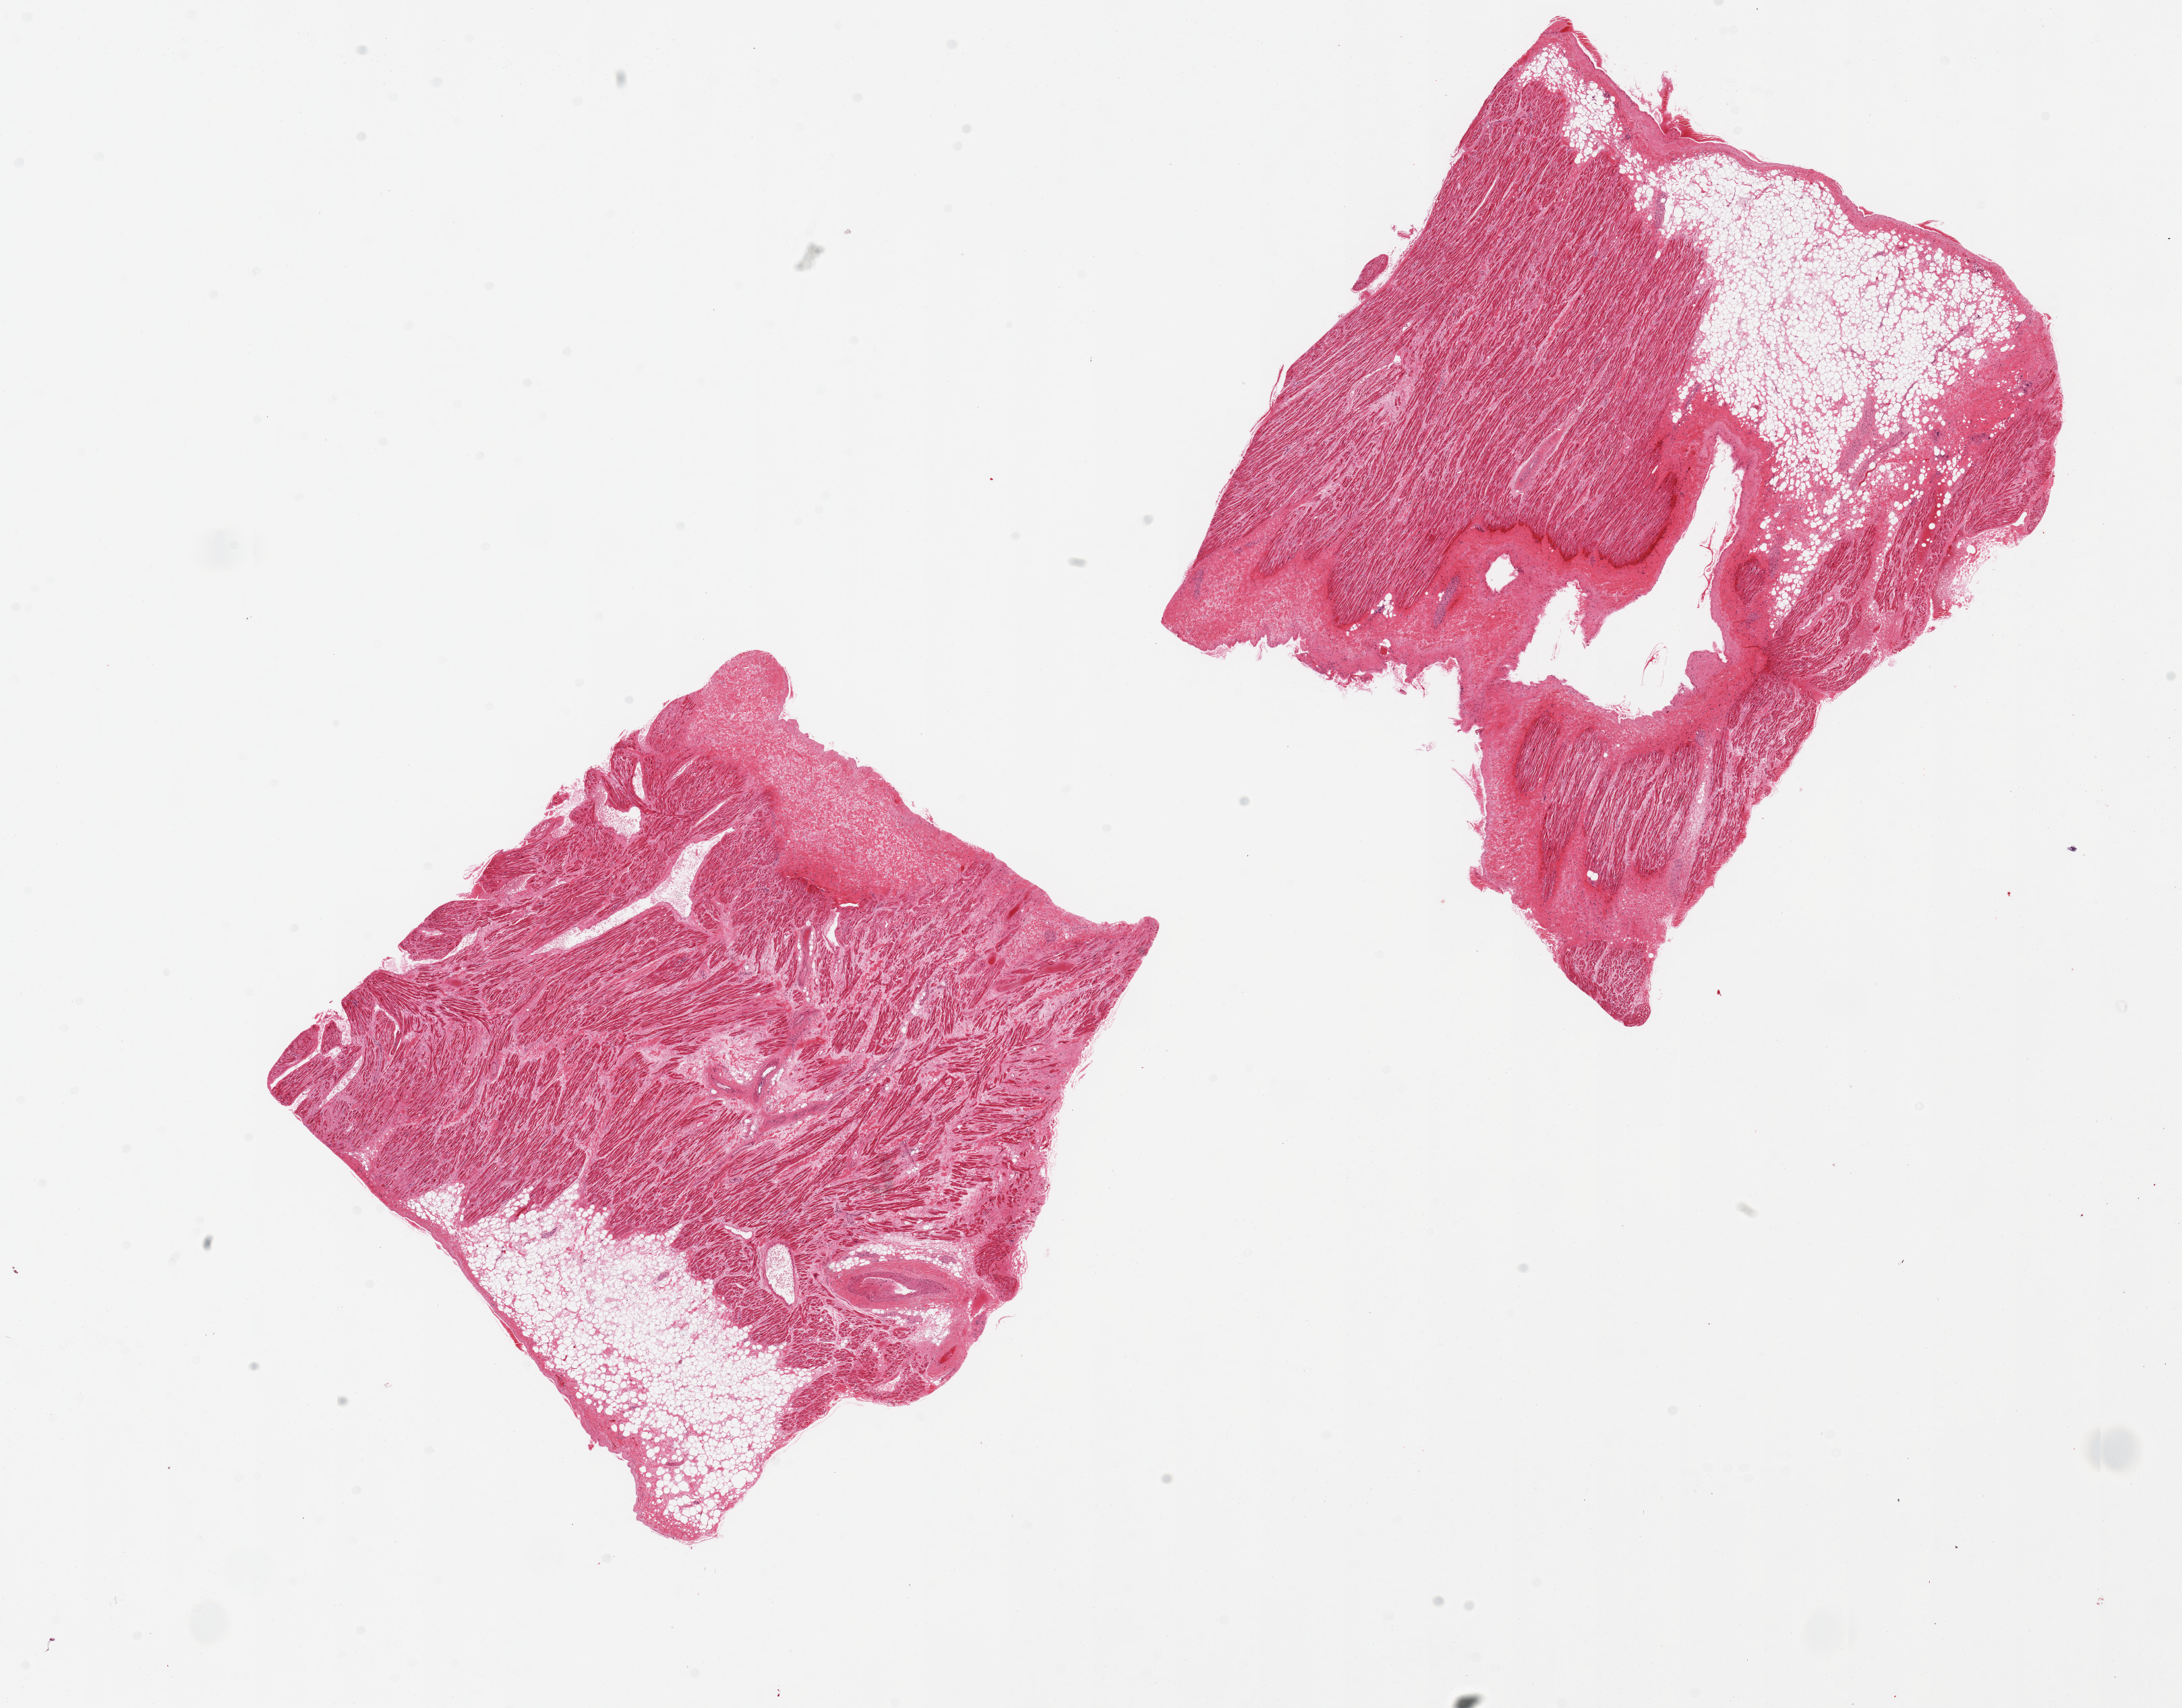
Whole-slide image, haematoxylin and eosin stain, brightfield — low-resolution overview of the scanned area, about 25.6 x 20.0 mm. Donor: male.
Specimen: PAXgene-fixed paraffin-embedded (PFPE) section; section of auricular appendage (target tissue); tissue donor sample.